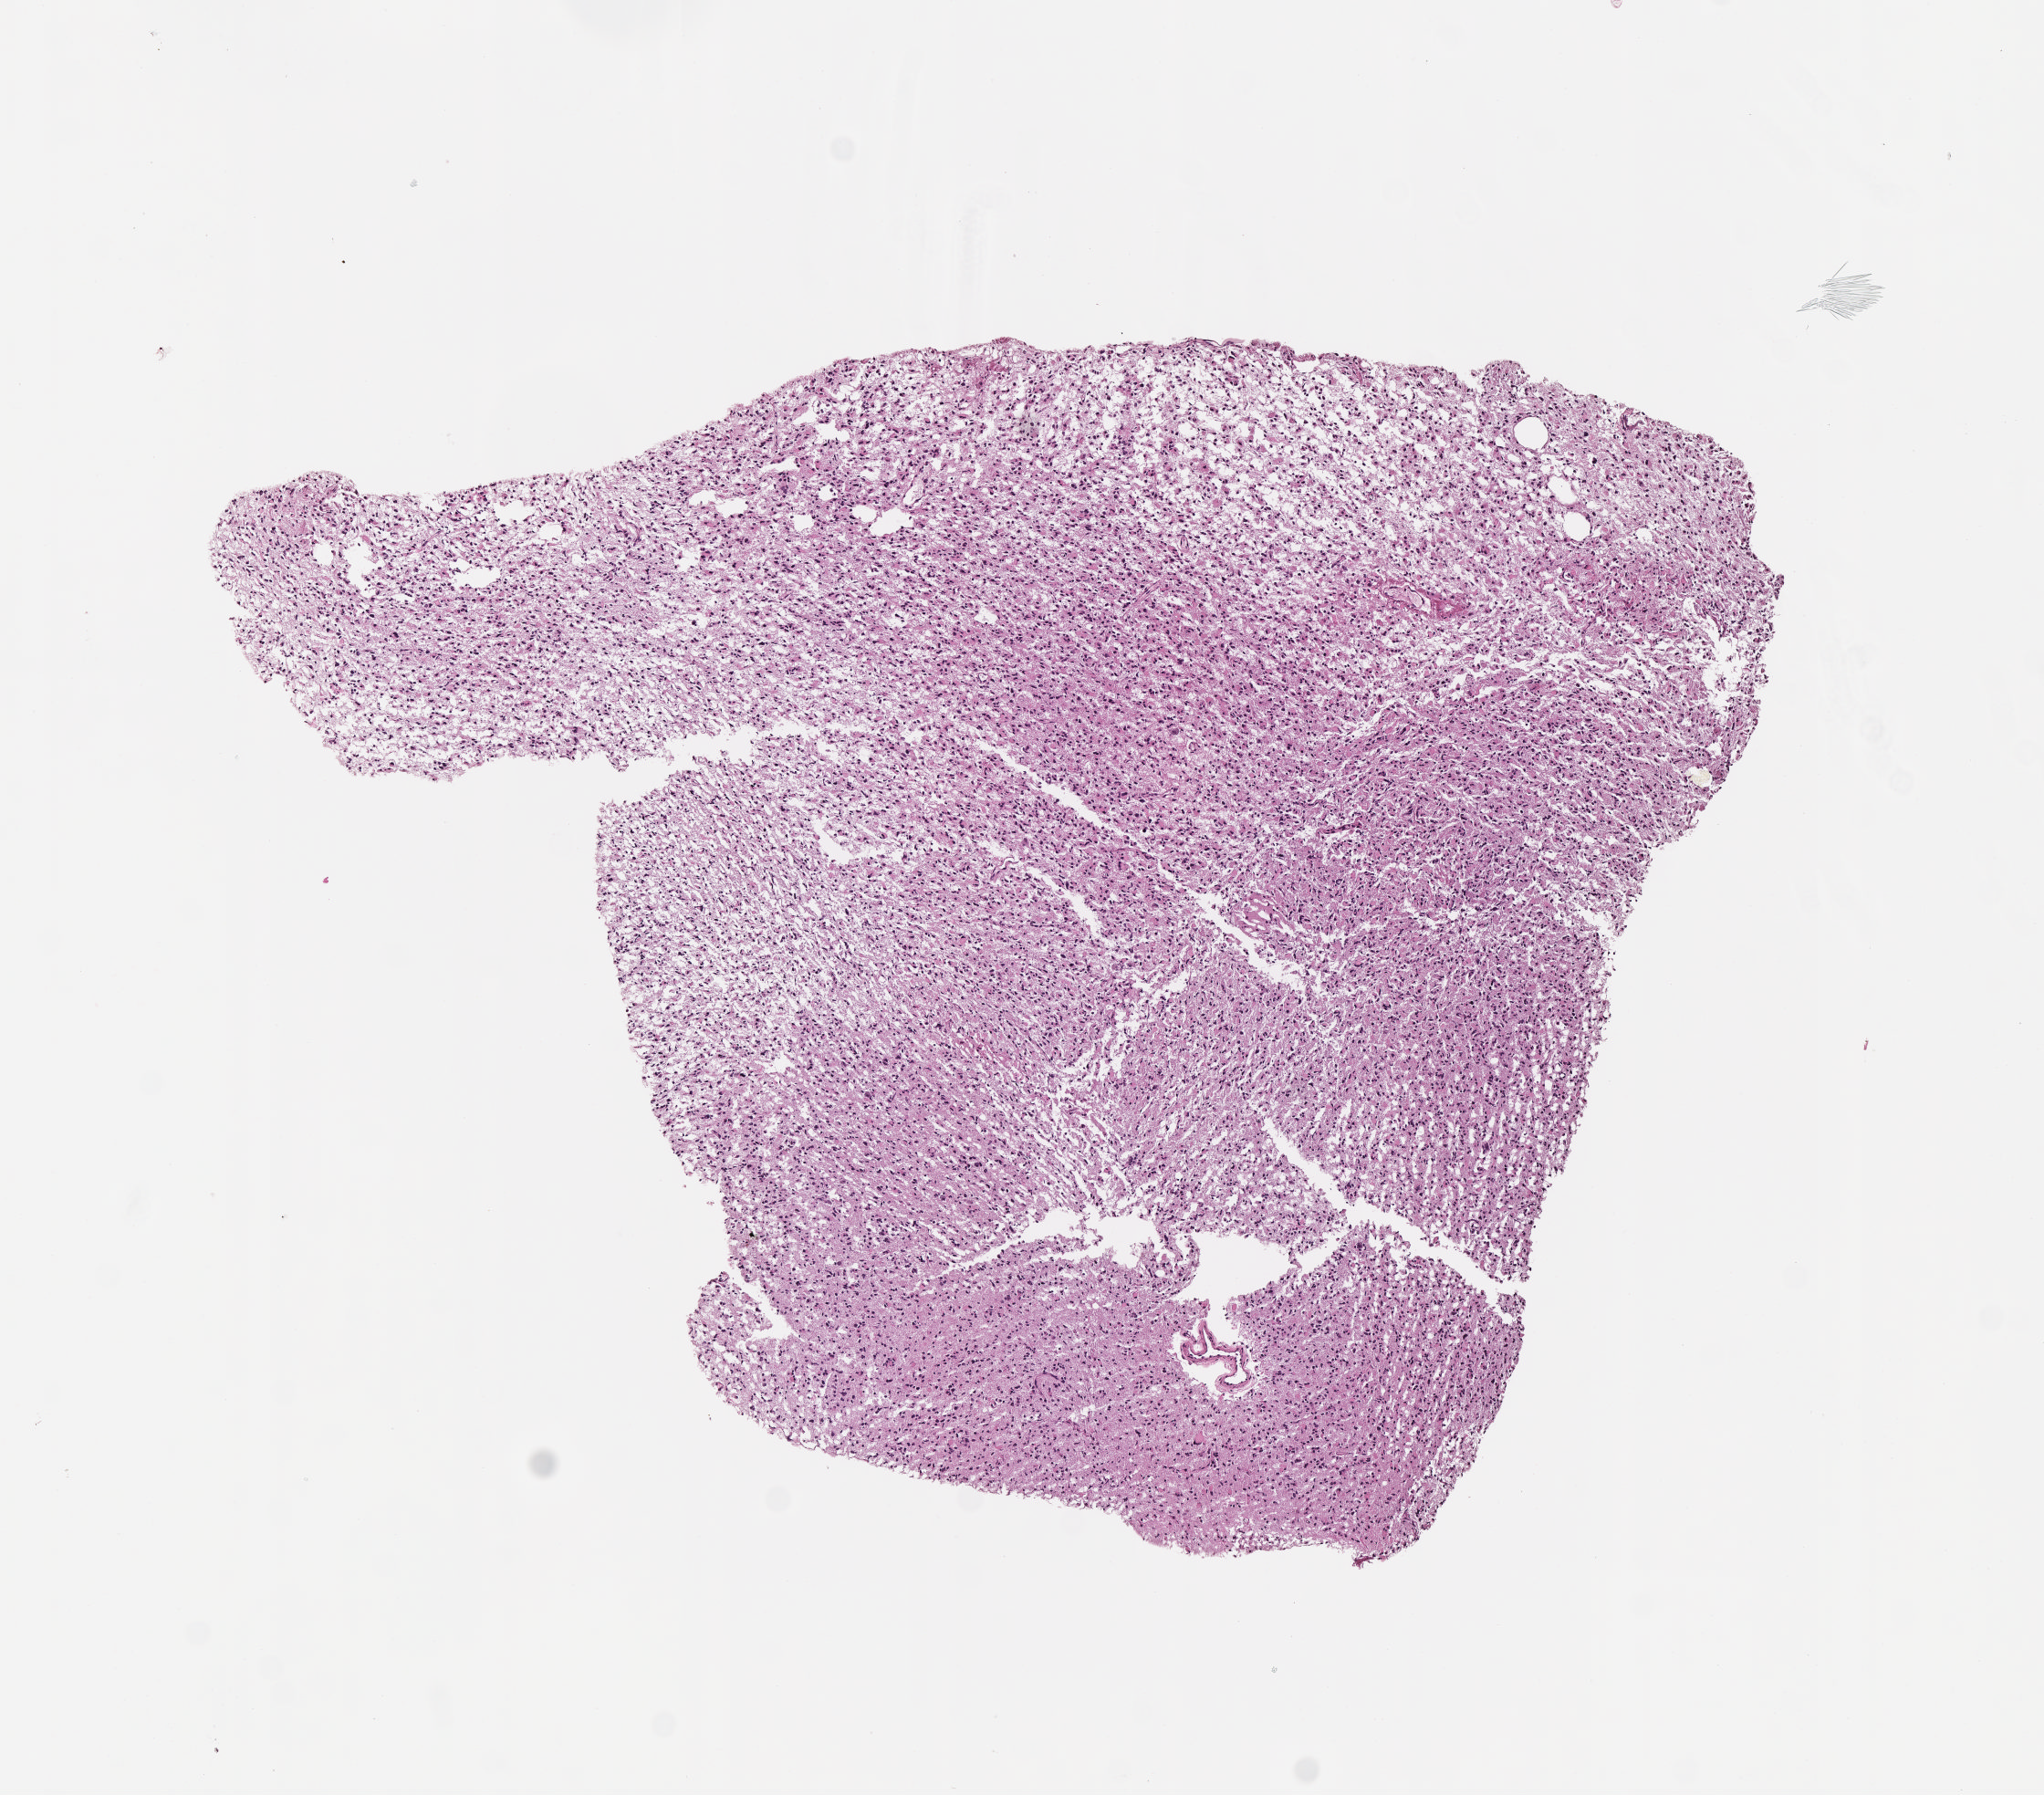
H&E-stained whole-slide image — shown as a low-resolution overview of the whole scanned area (about 4.5 x 4.0 mm). FFPE section. Primary tumour sample from the brain. Male patient; age at initial diagnosis 32 years. Histologic grade: G3 (poorly differentiated).
* histologic diagnosis: Astrocytoma, anaplastic (cerebrum)
* laterality: left